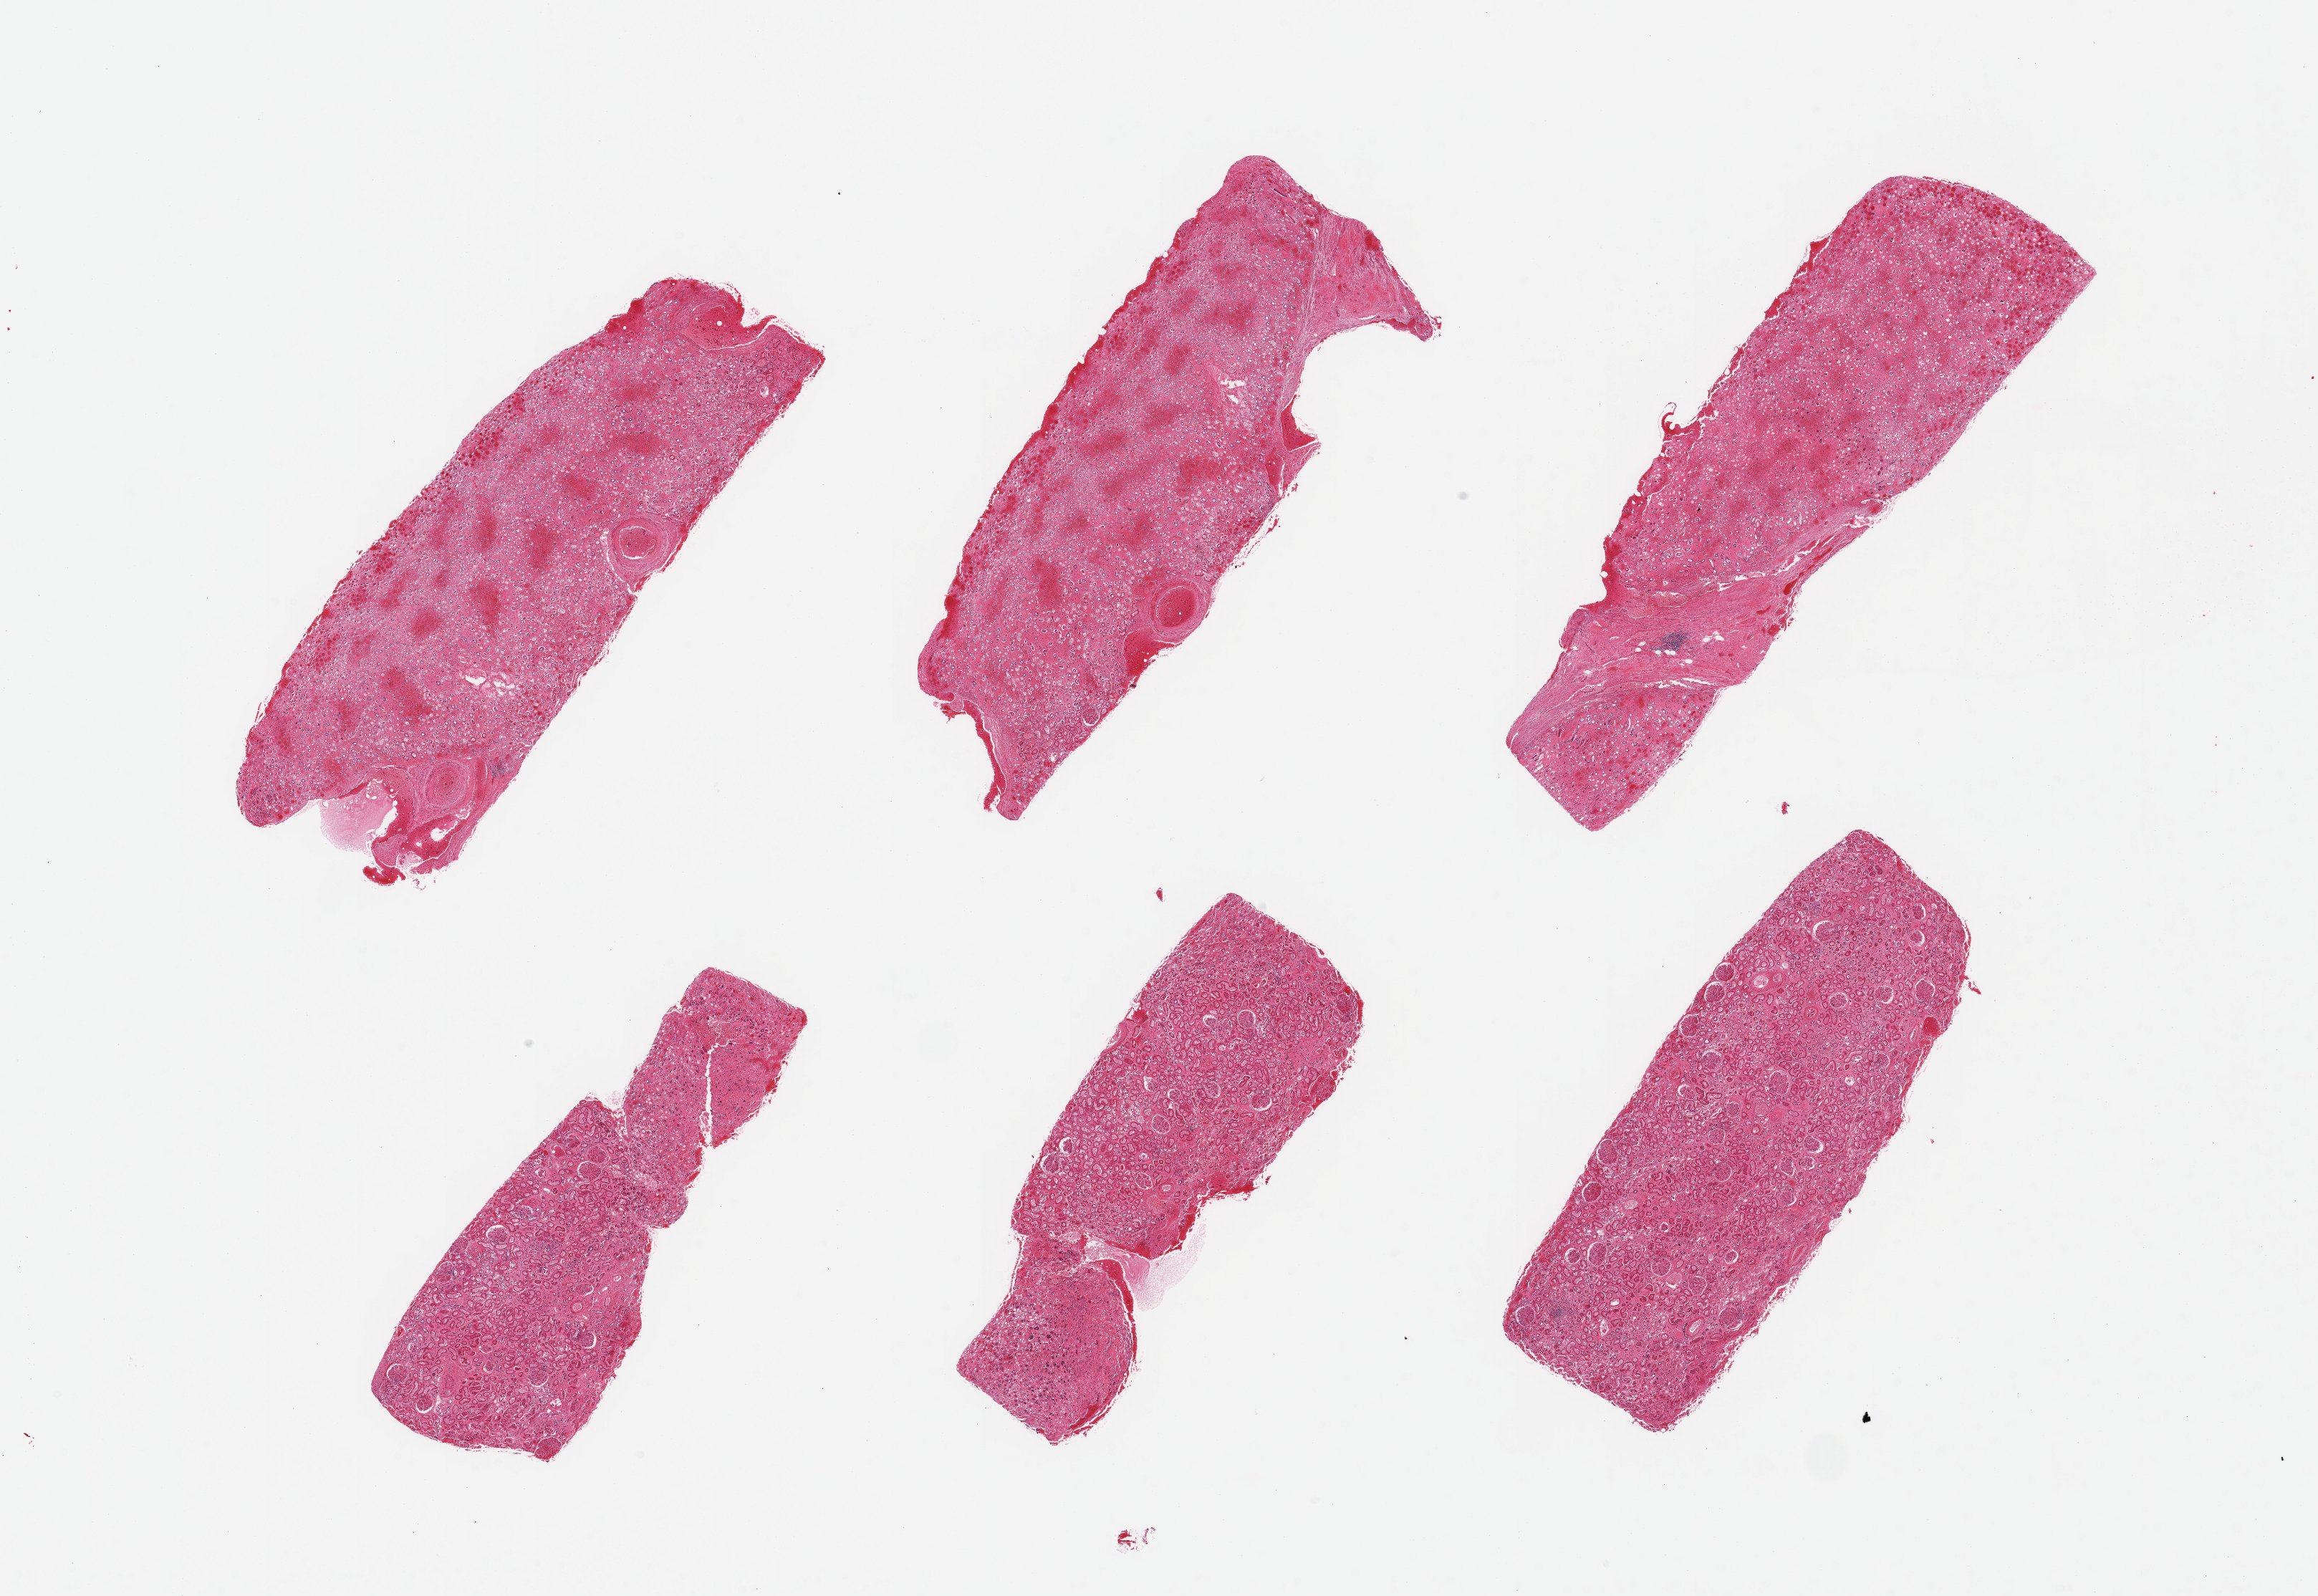
Digitized H&E-stained section, low-resolution overview of the scanned area, about 25.6 x 17.6 mm; PAXgene-fixed paraffin-embedded (PFPE) section; sampled site (target tissue): renal cortex; donor tissue sample. Male donor.
• pathologist's review note for this sample: 6 pieces, glomeruli present in 3; advanced autolysis